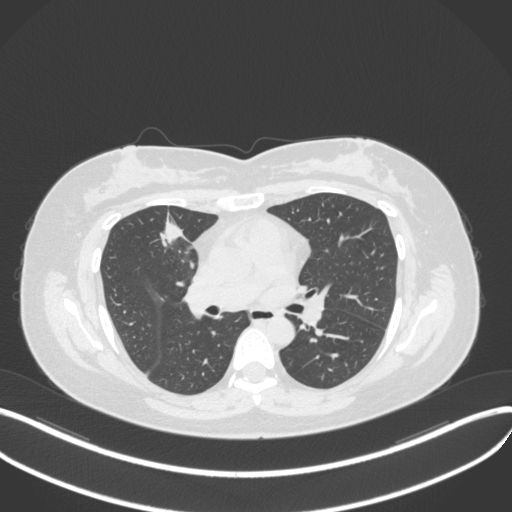
Chest CT, one axial slice; slice 176 of 272 in the series (ordered by position); reconstruction kernel B31f; lung window (W 1500 / L -600 HU); 1 mm slice thickness; 512 × 512 image matrix, field of view 400 × 400 mm. Patient: female, 42 years. Case-level facts recorded for this patient, not image findings: clinical TNM (as recorded): T1b N0 M0.
Outlined on this slice (rectangle marked by the reading radiologist):
- lung tumour (recorded histology: adenocarcinoma): box from (x=153, y=216) to (x=190, y=251) px